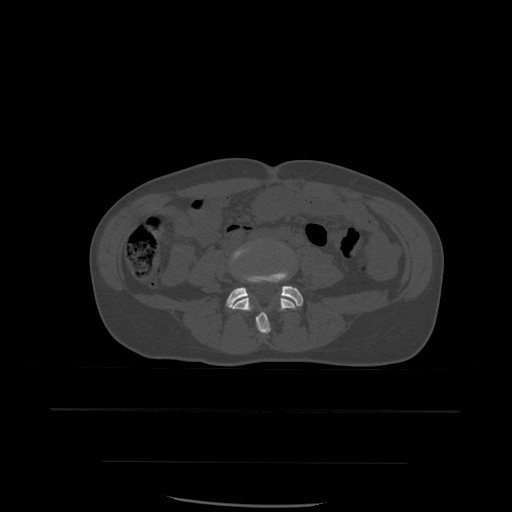
CT including the spine, one axial slice; position 160 of 574 along the scan axis; bone window (W 1800 / L 400 HU); 1.25 mm slice thickness; 512 × 512 image matrix, field of view 392 × 392 mm. Patient age 48 years. From the clinical record (not read from this slice): primary cancer: lung.
Outlined on this slice (semi-automatically segmented with operator editing):
- L4 vertebra: bounding box [x1, y1, x2, y2] px = [230, 243, 296, 334]
- L5 vertebra: [227, 272, 304, 309]